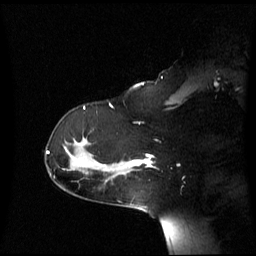
Breast MRI (dynamic contrast-enhanced), one sagittal slice; position 44 of 60 along the scan axis; dynamic contrast-enhanced series, image 2 of 3 at this slice position (ordered by acquisition); 1.5 T; TE 4.2 ms, TR 8.4 ms; 2.6 mm slice thickness; 256 × 256 image matrix, field of view 270 × 270 mm. Patient: female, 39 years. From the clinical record (not read from this slice): setting: breast cancer imaged before/during neoadjuvant chemotherapy; receptor status: triple-negative.
Outlined on this slice (semi-automatic segmentation, software-assisted and operator-edited):
- analysis volume of interest (the breast-tissue region the enhancement analysis was run in; not a lesion): bounding box <117,154,152,176> (left, top, right, bottom; pixels)
- tumour enhancement mask (voxels above the 70 % enhancement threshold inside the analysis volume of interest): <132,154,152,167>